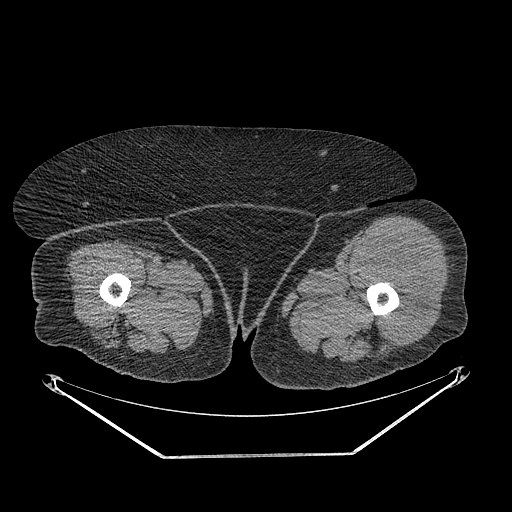
CT of an extremity soft-tissue mass (from a PET/CT study), one axial slice; position 248 of 267 along the scan axis; reconstruction kernel STANDARD; soft-tissue window (W 400 / L 40 HU); 3.75 mm slice thickness; 512 × 512 image matrix, field of view 500 × 500 mm. Female patient. From the clinical record (not read from this slice): histological type: undifferentiated – high grade; grade: high; site of the primary tumour: left thigh.
Annotated regions visible in this slice (expert contour drawn on MRI and transferred to this co-registered scan by the dataset authors):
- gross tumour volume including surrounding oedema: bounding box <361,237,432,343> (left, top, right, bottom; pixels)
- gross tumour volume (mass): <363,242,430,343>